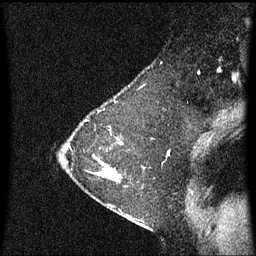
Breast MRI (dynamic contrast-enhanced), one sagittal slice; dynamic contrast-enhanced series, image 2 of 3 at this slice position (ordered by acquisition); 1.5 T; TE 4.2 ms, TR 8.4 ms; 2 mm slice thickness; 256 × 256 image matrix, field of view 200 × 200 mm. Patient: female, 36 years. Case-level facts recorded for this patient, not image findings: setting: breast cancer imaged before/during neoadjuvant chemotherapy; receptor status: HR-positive, HER2-negative.
Outlined on this slice (semi-automatic segmentation, software-assisted and operator-edited):
- analysis volume of interest (the breast-tissue region the enhancement analysis was run in; not a lesion): box from (x=72, y=116) to (x=123, y=185) px
- tumour enhancement mask (voxels above the 70 % enhancement threshold inside the analysis volume of interest): (x=104, y=166)–(x=117, y=181)